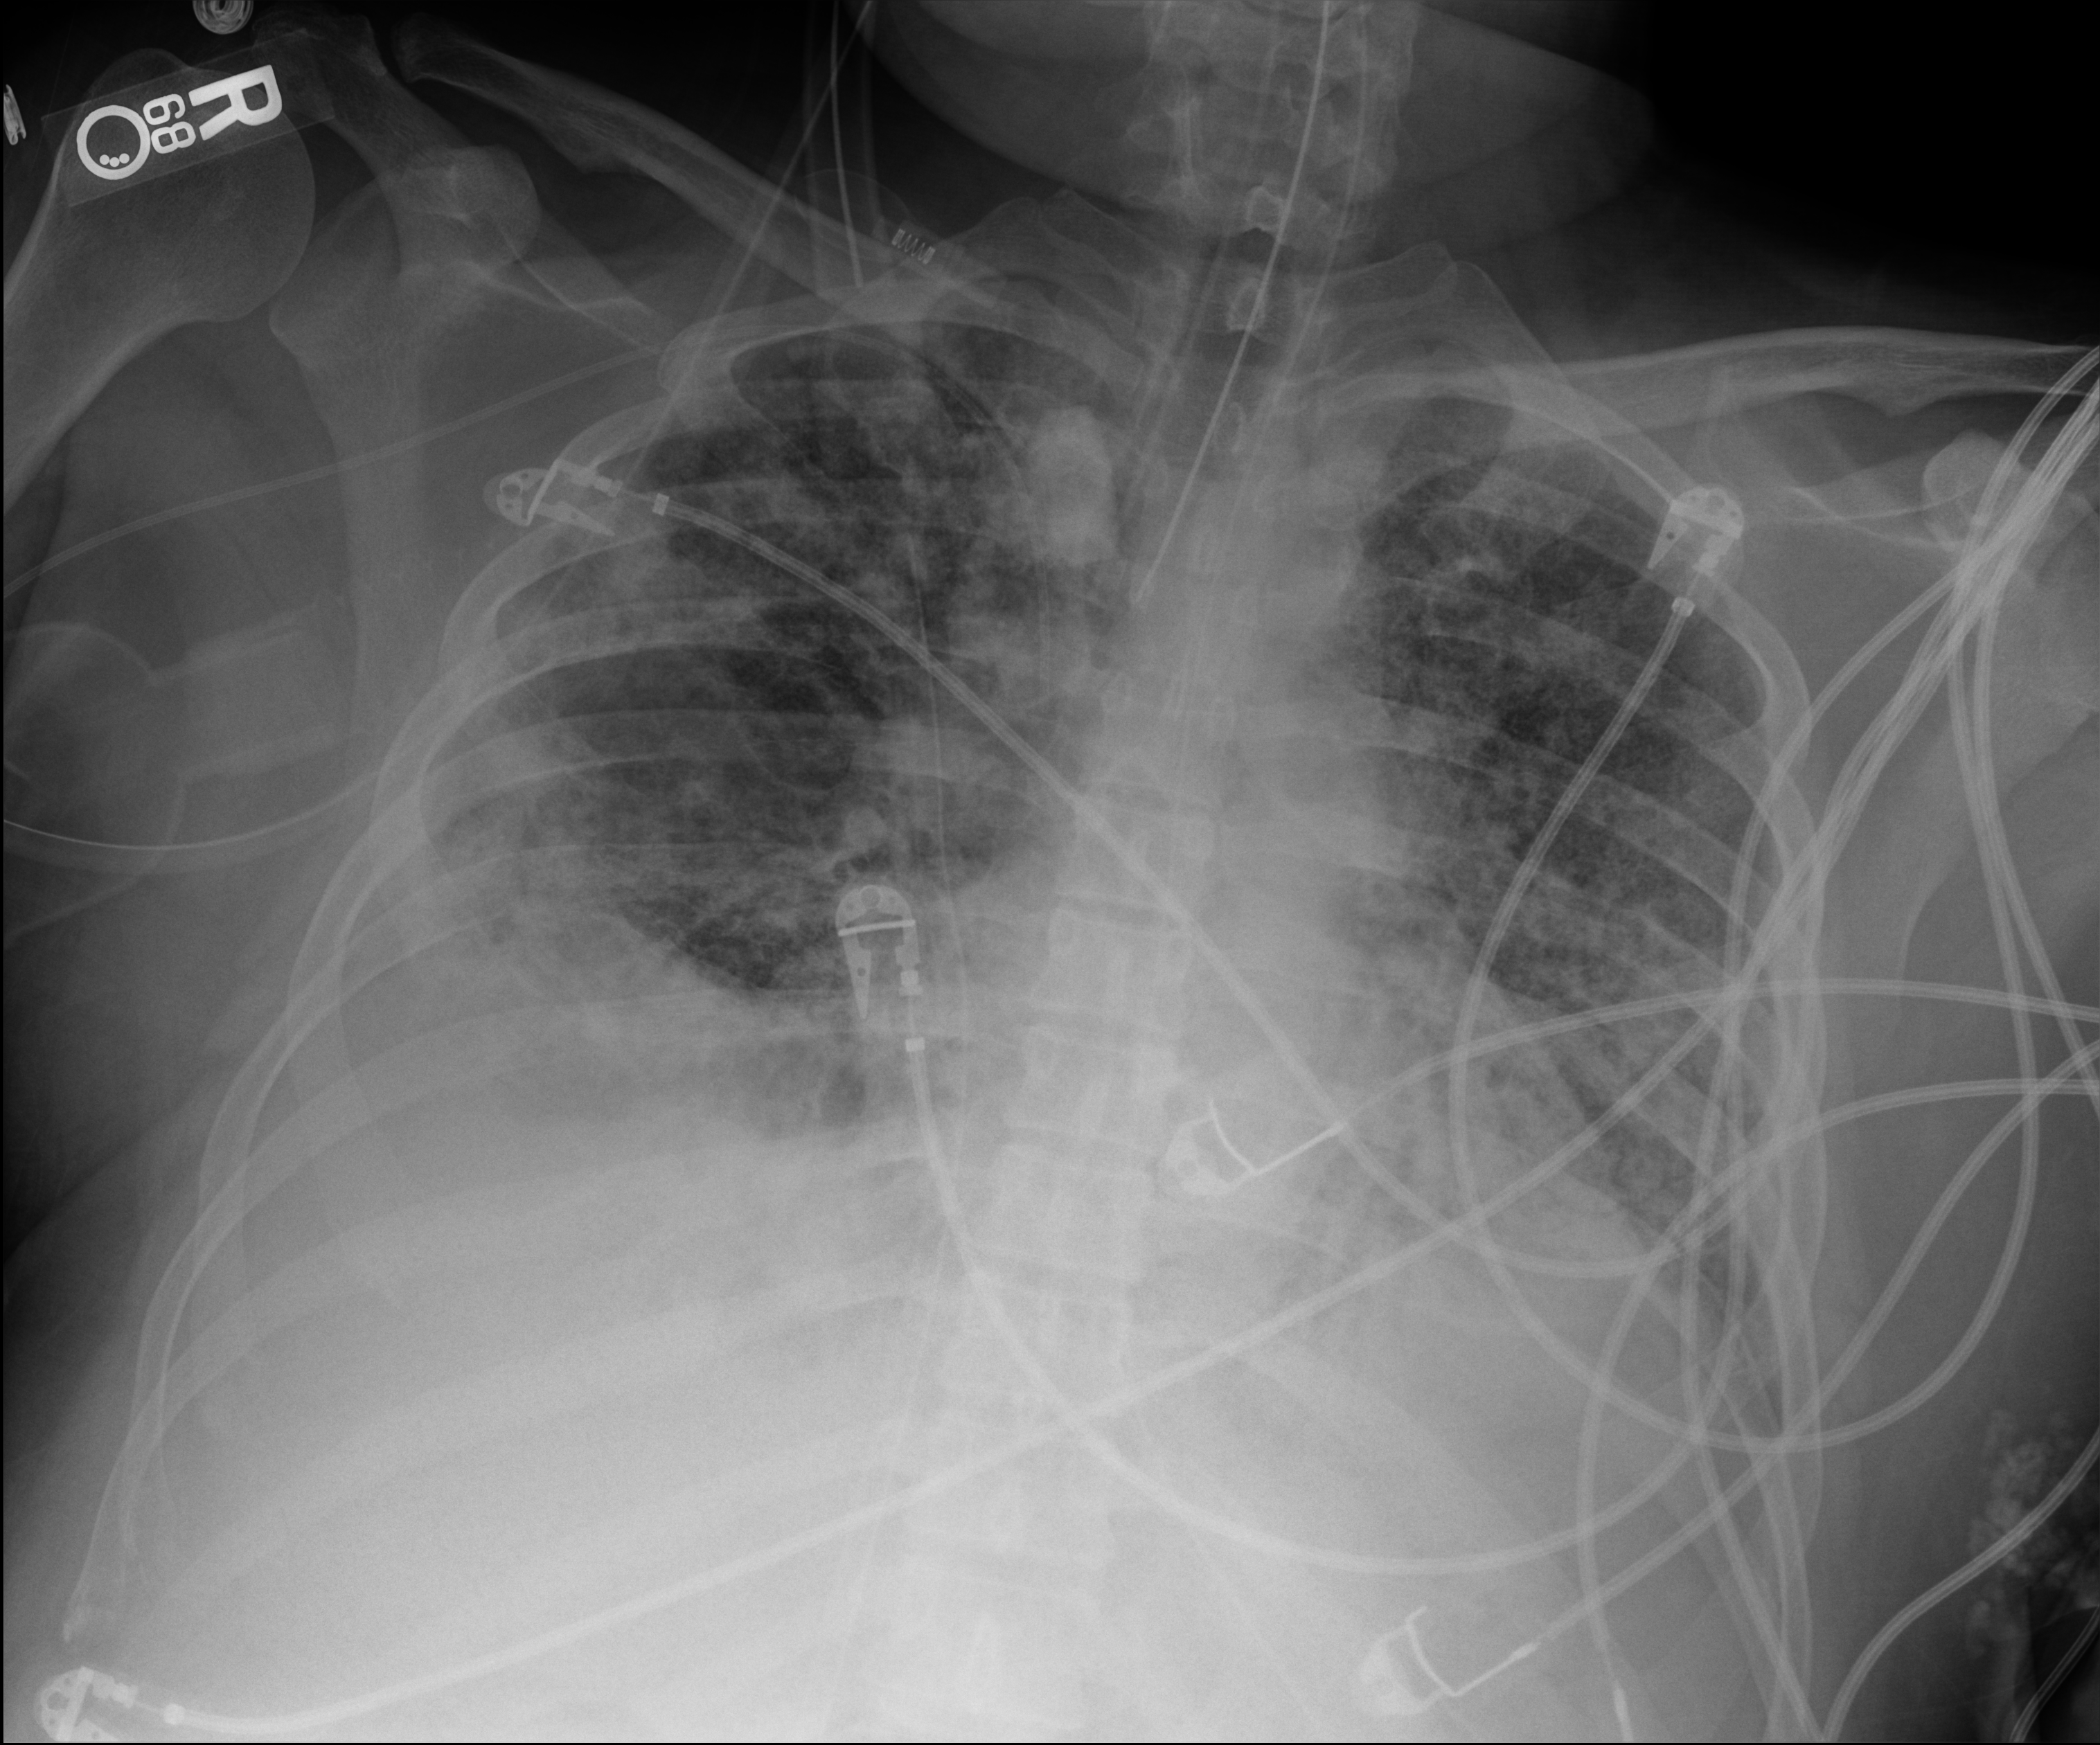
Chest X-ray (portable), anteroposterior (AP) projection. Patient hospitalised with COVID-19; male, aged 18–59 years.
From the hospital-stay record, not from the radiograph (when in the stay this image was taken is not recorded): admitted to intensive care during this hospital stay: yes; length of hospital stay: 96 days; COPD (admission record): no.